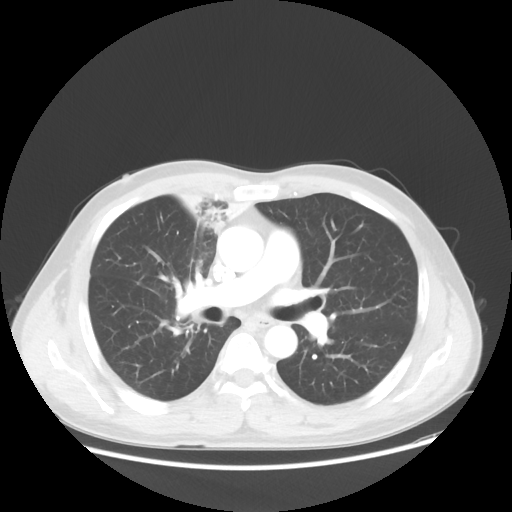
Chest CT, one axial slice. Slice 31 of 56 in the series (ordered by position). 100 kVp. Lung window (W 1500 / L -600 HU). 512 × 512 image matrix, field of view 398 × 398 mm. Male patient, age 60 years. Case-level facts recorded for this patient, not image findings: clinical TNM (as recorded): T2a N1 M0.
Structures marked on this image (rectangle marked by the reading radiologist):
- lung tumour (recorded histology: squamous cell carcinoma): bounding box [x1, y1, x2, y2] px = [157, 174, 262, 237]